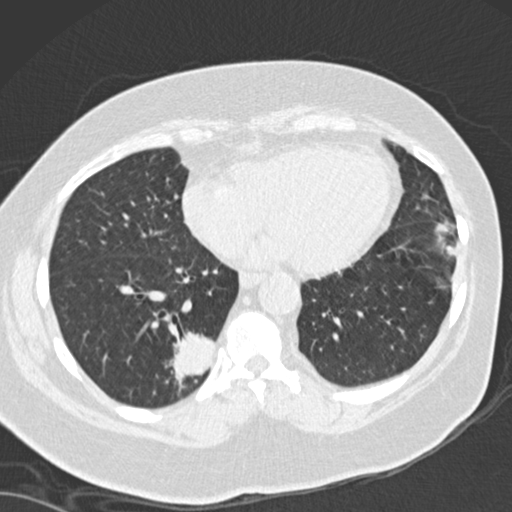
Low-dose screening chest CT, one axial slice. Slice 57 of 162 in the series (ordered by position). Reconstruction kernel B30f. 120 kVp. Lung window (W 1500 / L -600 HU). 512 × 512 image matrix, field of view 328 × 328 mm.
Annotated regions visible in this slice (outlined manually by an expert reader):
- lesion 1 (tumor, lower lobe of right lung): bounding box <173,332,214,389> (left, top, right, bottom; pixels)